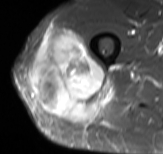
MRI of an extremity soft-tissue mass, one axial slice; position 43 of 61 along the scan axis; STIR; MR volume resampled by the dataset authors to the PET/CT grid (not the native acquisition matrix); 3.27 mm slice thickness; 163 × 154 image matrix, field of view 159 × 150 mm. Male patient. Case-level facts recorded for this patient, not image findings: histological type: poorly differentiated synovial sarcoma; grade: high; site of the primary tumour: right buttock.
Annotated regions visible in this slice (expert contour drawn on MRI and transferred to this co-registered scan by the dataset authors):
- gross tumour volume including surrounding oedema: bounding box (x1, y1, x2, y2) in pixels: (29, 25, 111, 122)
- gross tumour volume (mass): (29, 27, 108, 122)